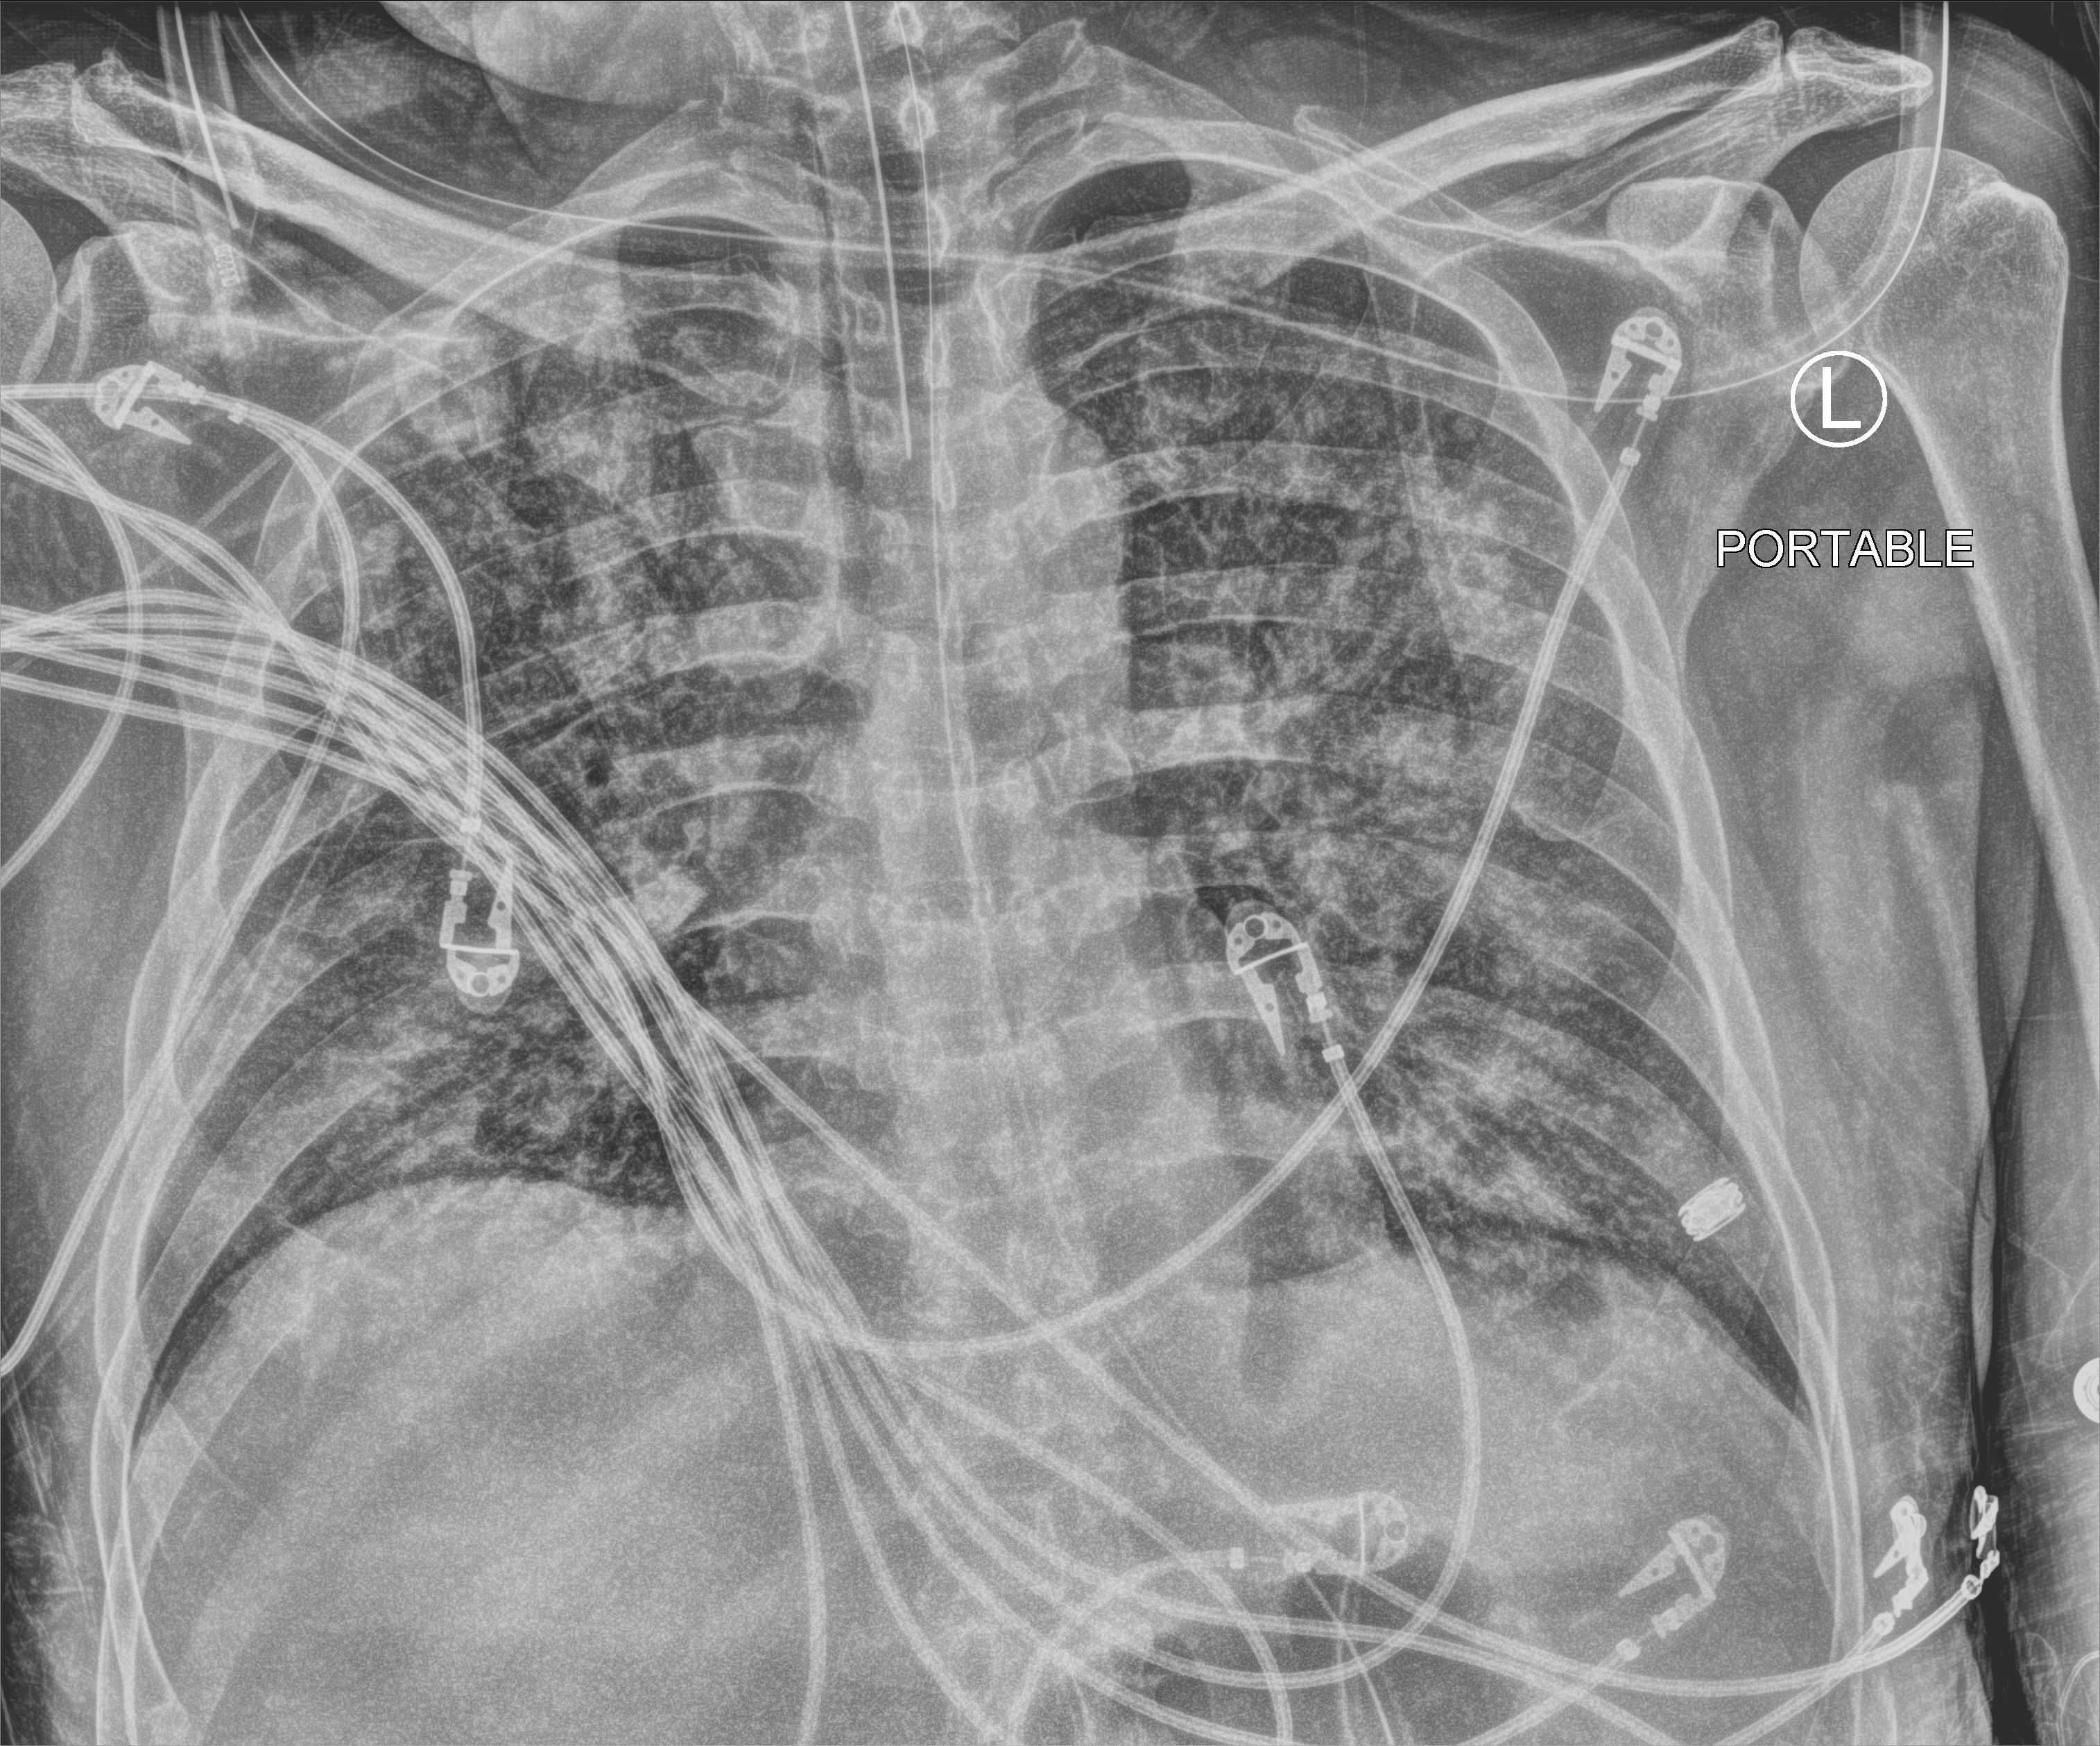
Portable chest radiograph; anteroposterior (AP) projection. Male patient hospitalised with COVID-19, age 18–59 years.
From the hospital-stay record, not from the radiograph (when in the stay this image was taken is not recorded): length of hospital stay: 40 days; admitted to intensive care during this hospital stay: yes.